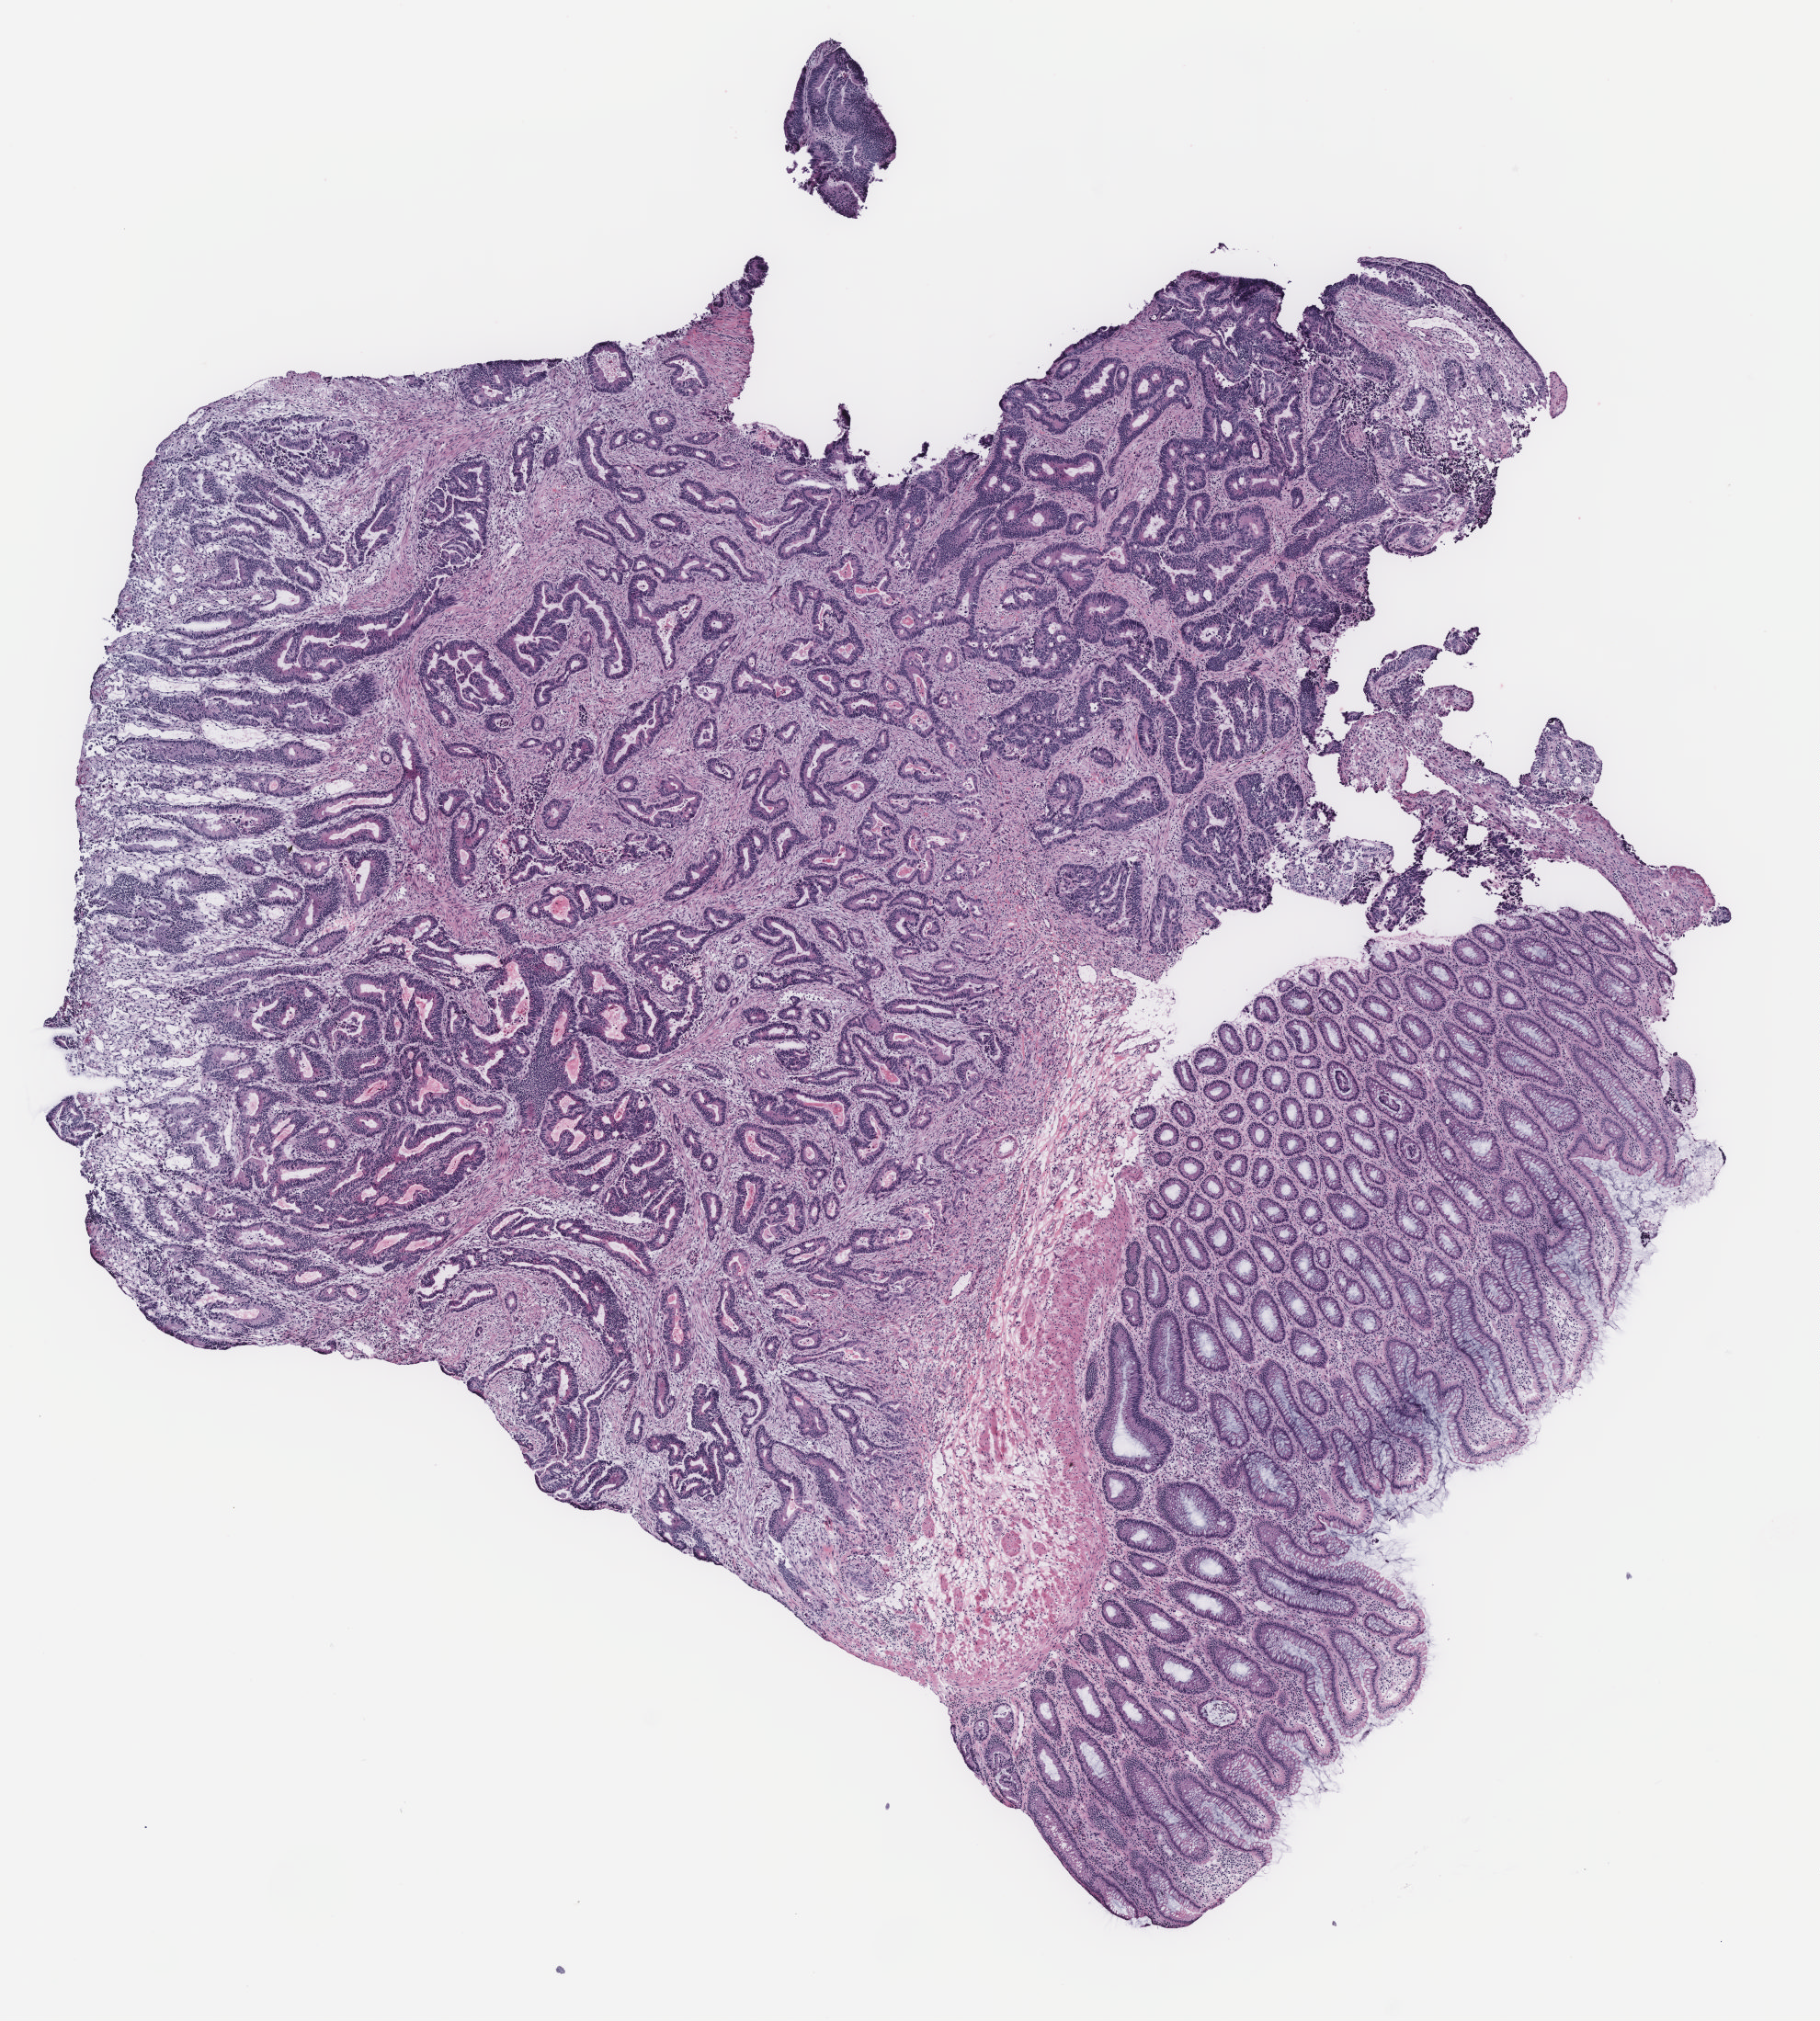
Digitized Hematoxylin and eosin (H&E) stained tissue section (whole slide) — shown as a low-resolution overview of the whole scanned area (about 7.9 x 8.8 mm, from a 40x scan); colon, tissue type not recorded.
Patient diagnosis (cohort enrolment): colon cancer (colon).